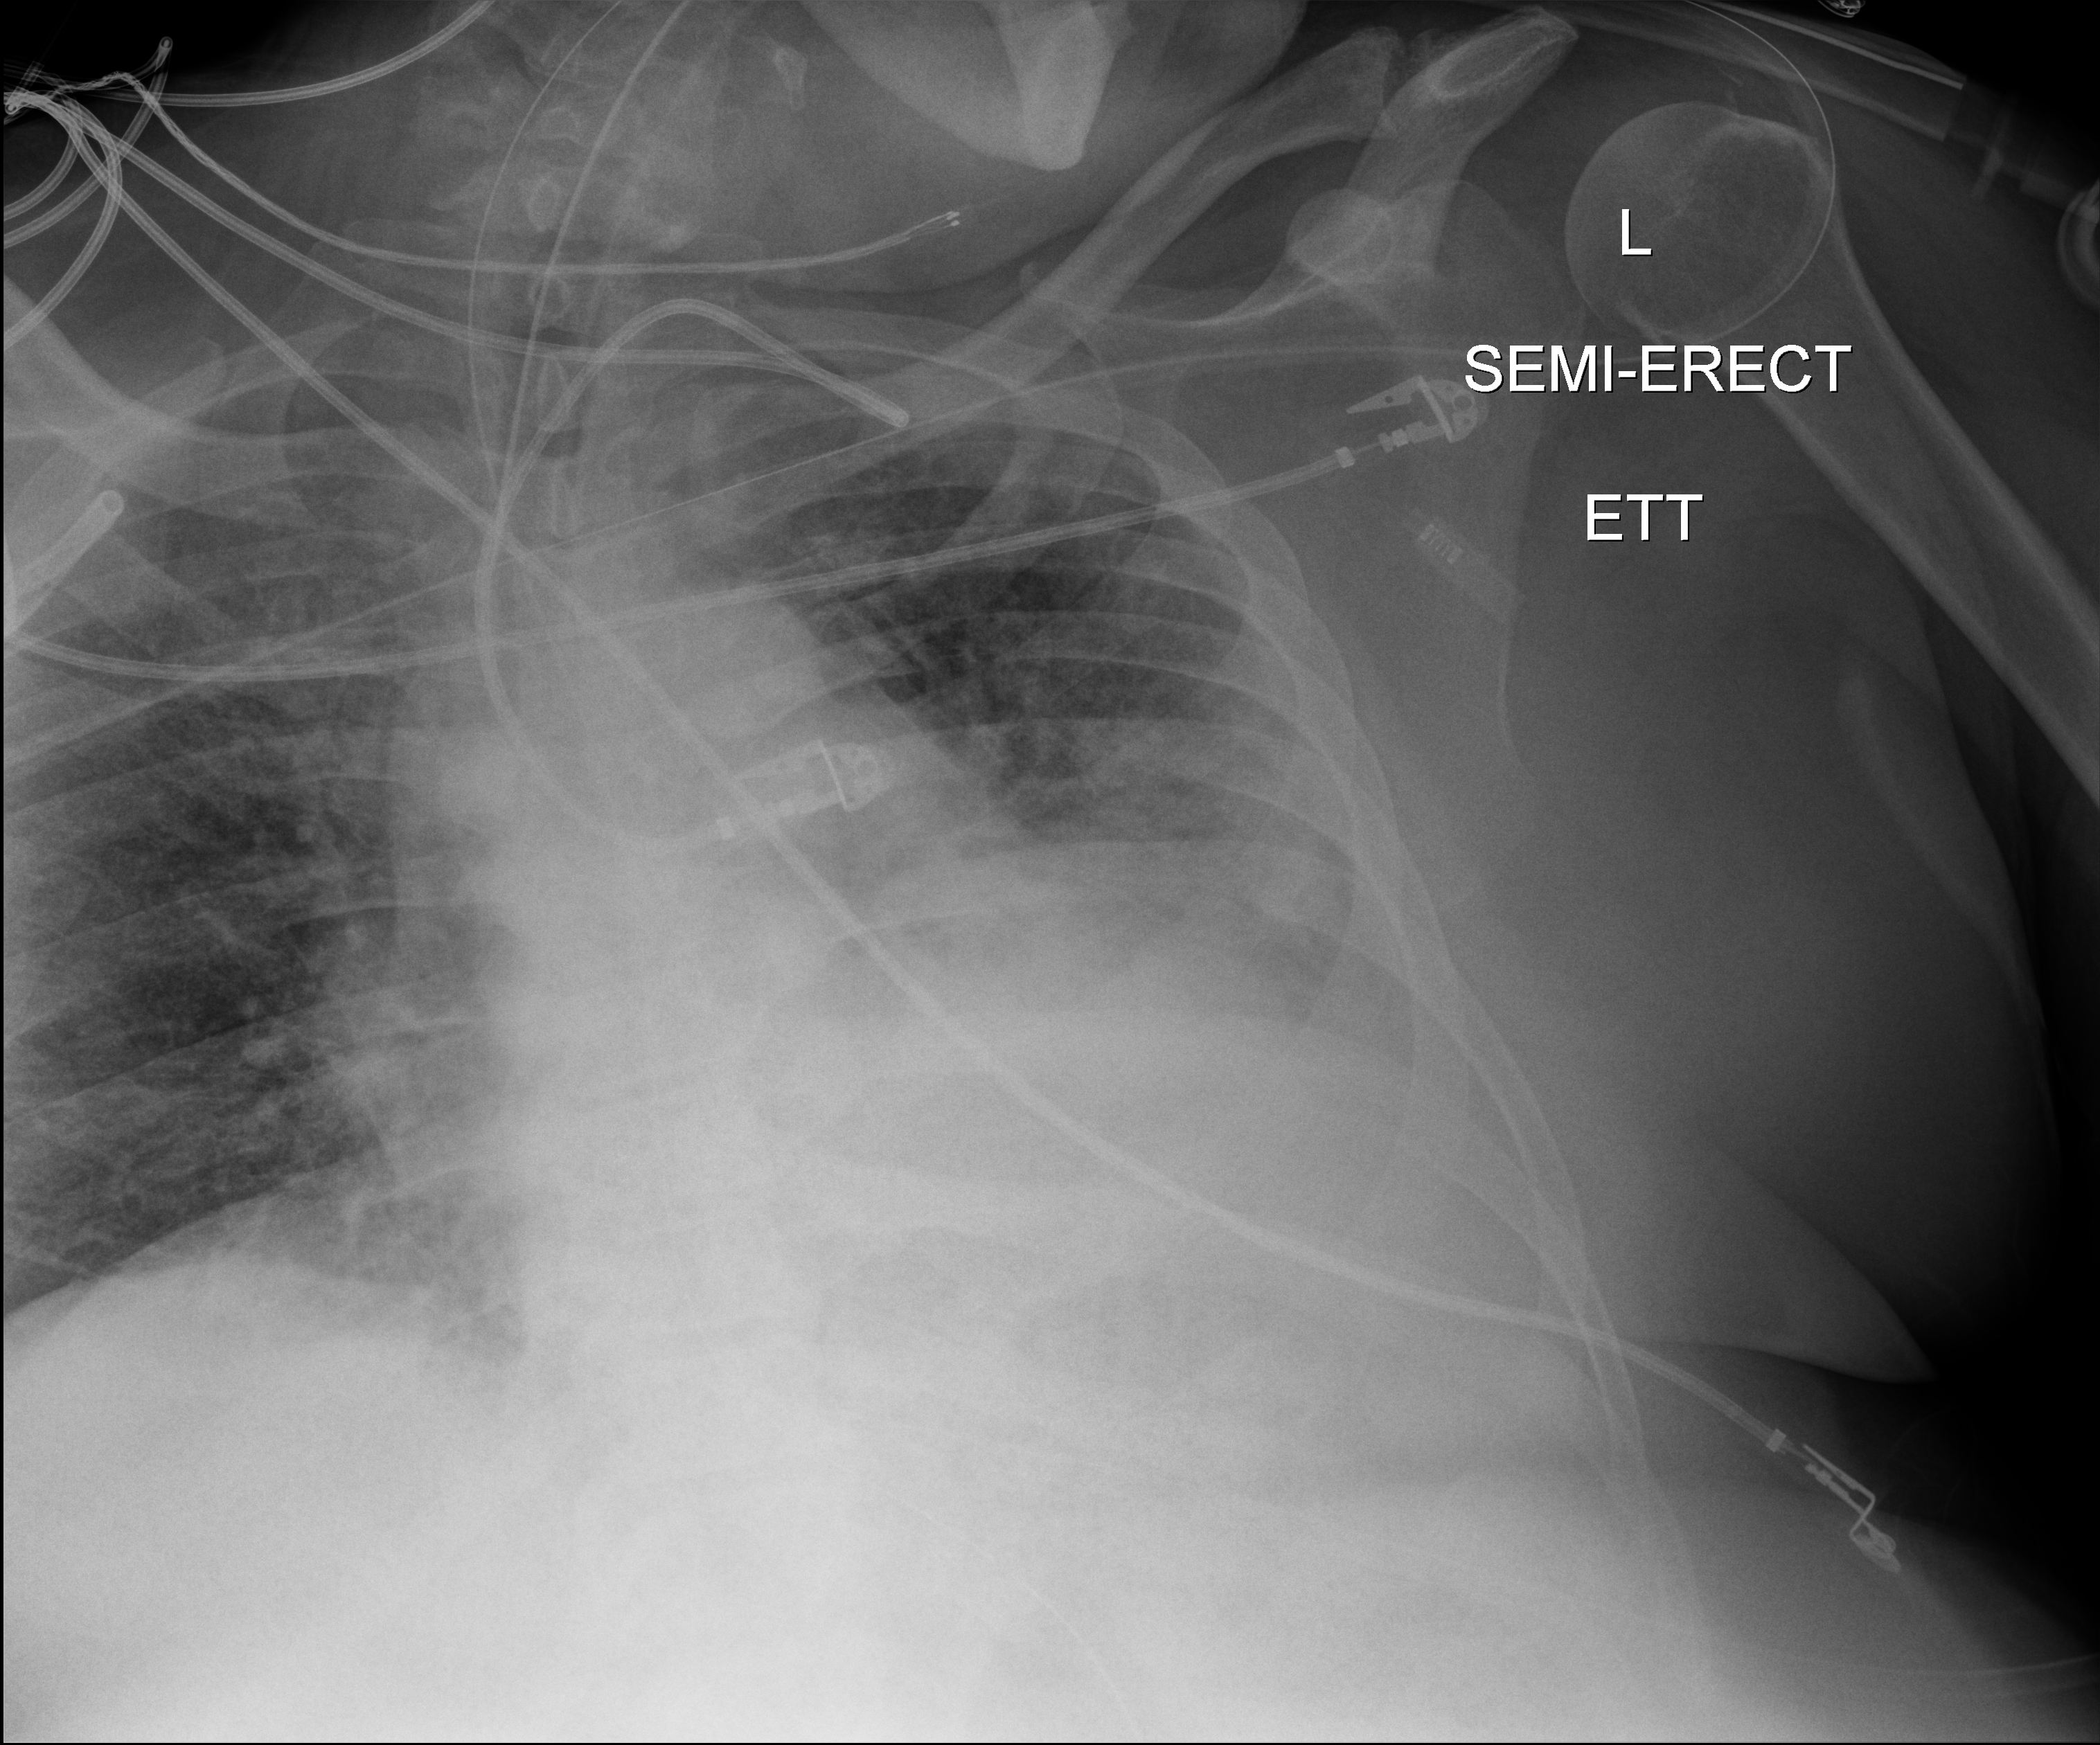
Chest X-ray; anteroposterior (AP) projection. Male patient hospitalised with COVID-19, age 60–74 years.
Admission-level facts for this patient (not findings on this image; timing relative to this image not recorded): admitted to intensive care during this hospital stay: yes; length of hospital stay: 34 days; mechanically ventilated during this hospital stay: yes.